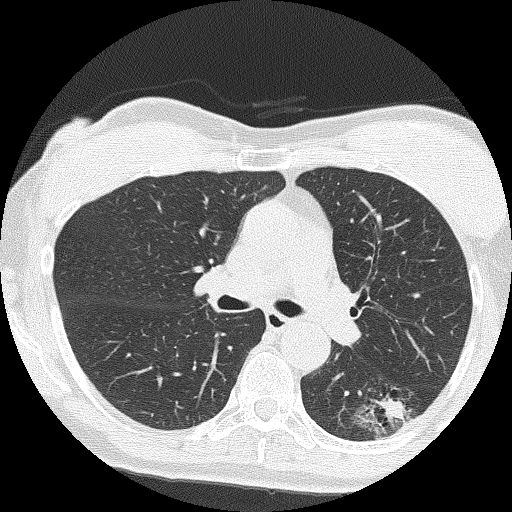
Chest CT (low-dose screening protocol), one axial image. Second screening round (one year after baseline). Lung window (W 1500 / L -600 HU). 2 mm slice thickness. Lung (sharp) reconstruction kernel (FC51). 120 kVp. 512 × 512 image matrix. Female, age 64 years at enrolment. Former smoker at enrolment.
• Lesion marked by an expert reader, box from (x=356, y=378) to (x=429, y=439) px.
• The screening reader recorded 3 non-calcified nodules or masses ≥4 mm on this exam (right upper lobe, right upper lobe, right middle lobe); which of them this box marks is not recorded.